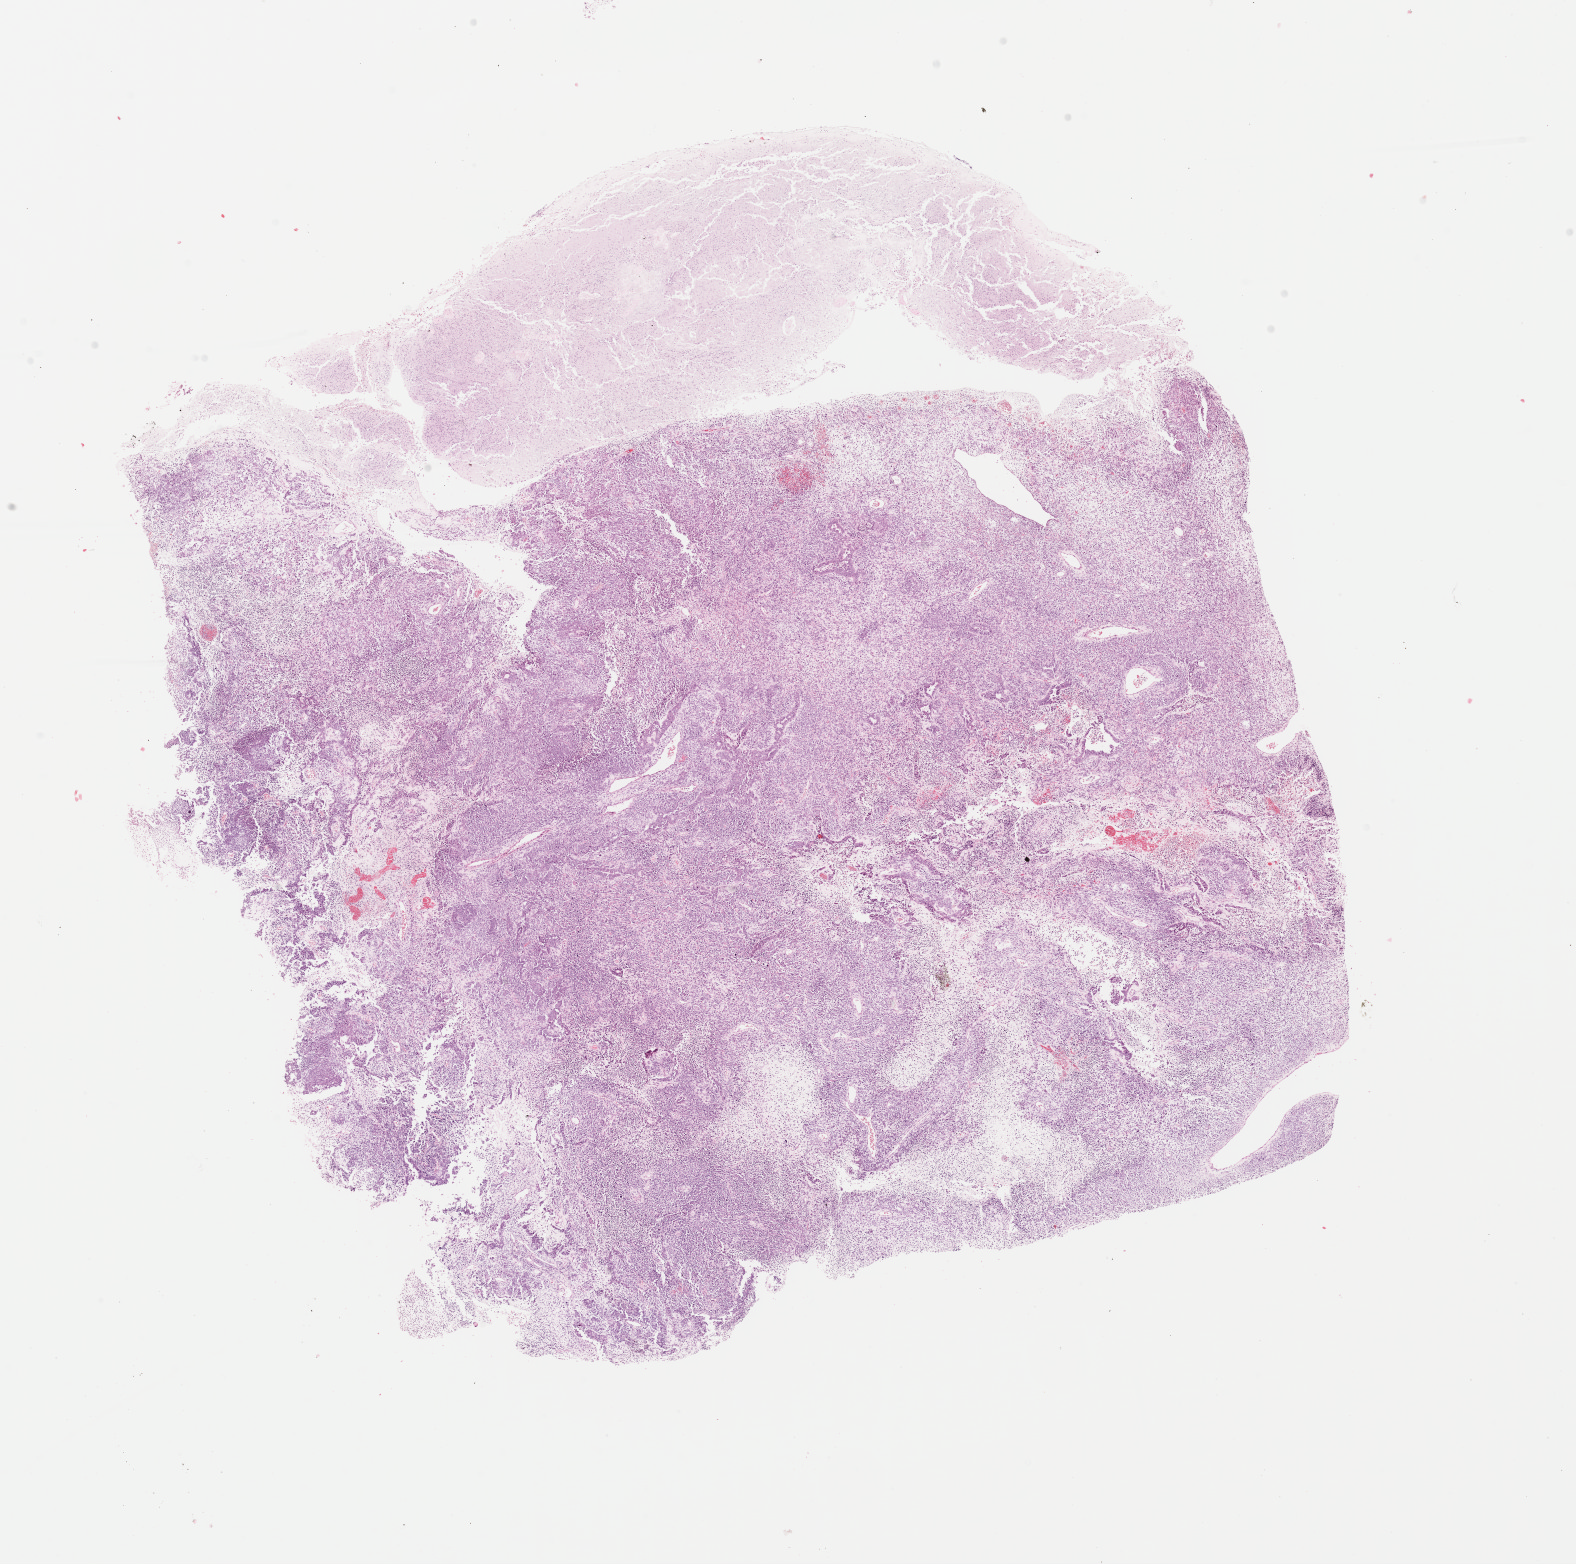
Whole-slide histology image, Hematoxylin and eosin (H&E) stained, low-resolution overview of the scanned area, about 12.5 x 12.4 mm. FFPE section. Sample: primary tumour, uterus. Female patient; age at initial diagnosis 70 years.
* lymph nodes positive (case pathology): 0 of 4 examined
* FIGO stage: II
* diagnosis: Mullerian mixed tumor